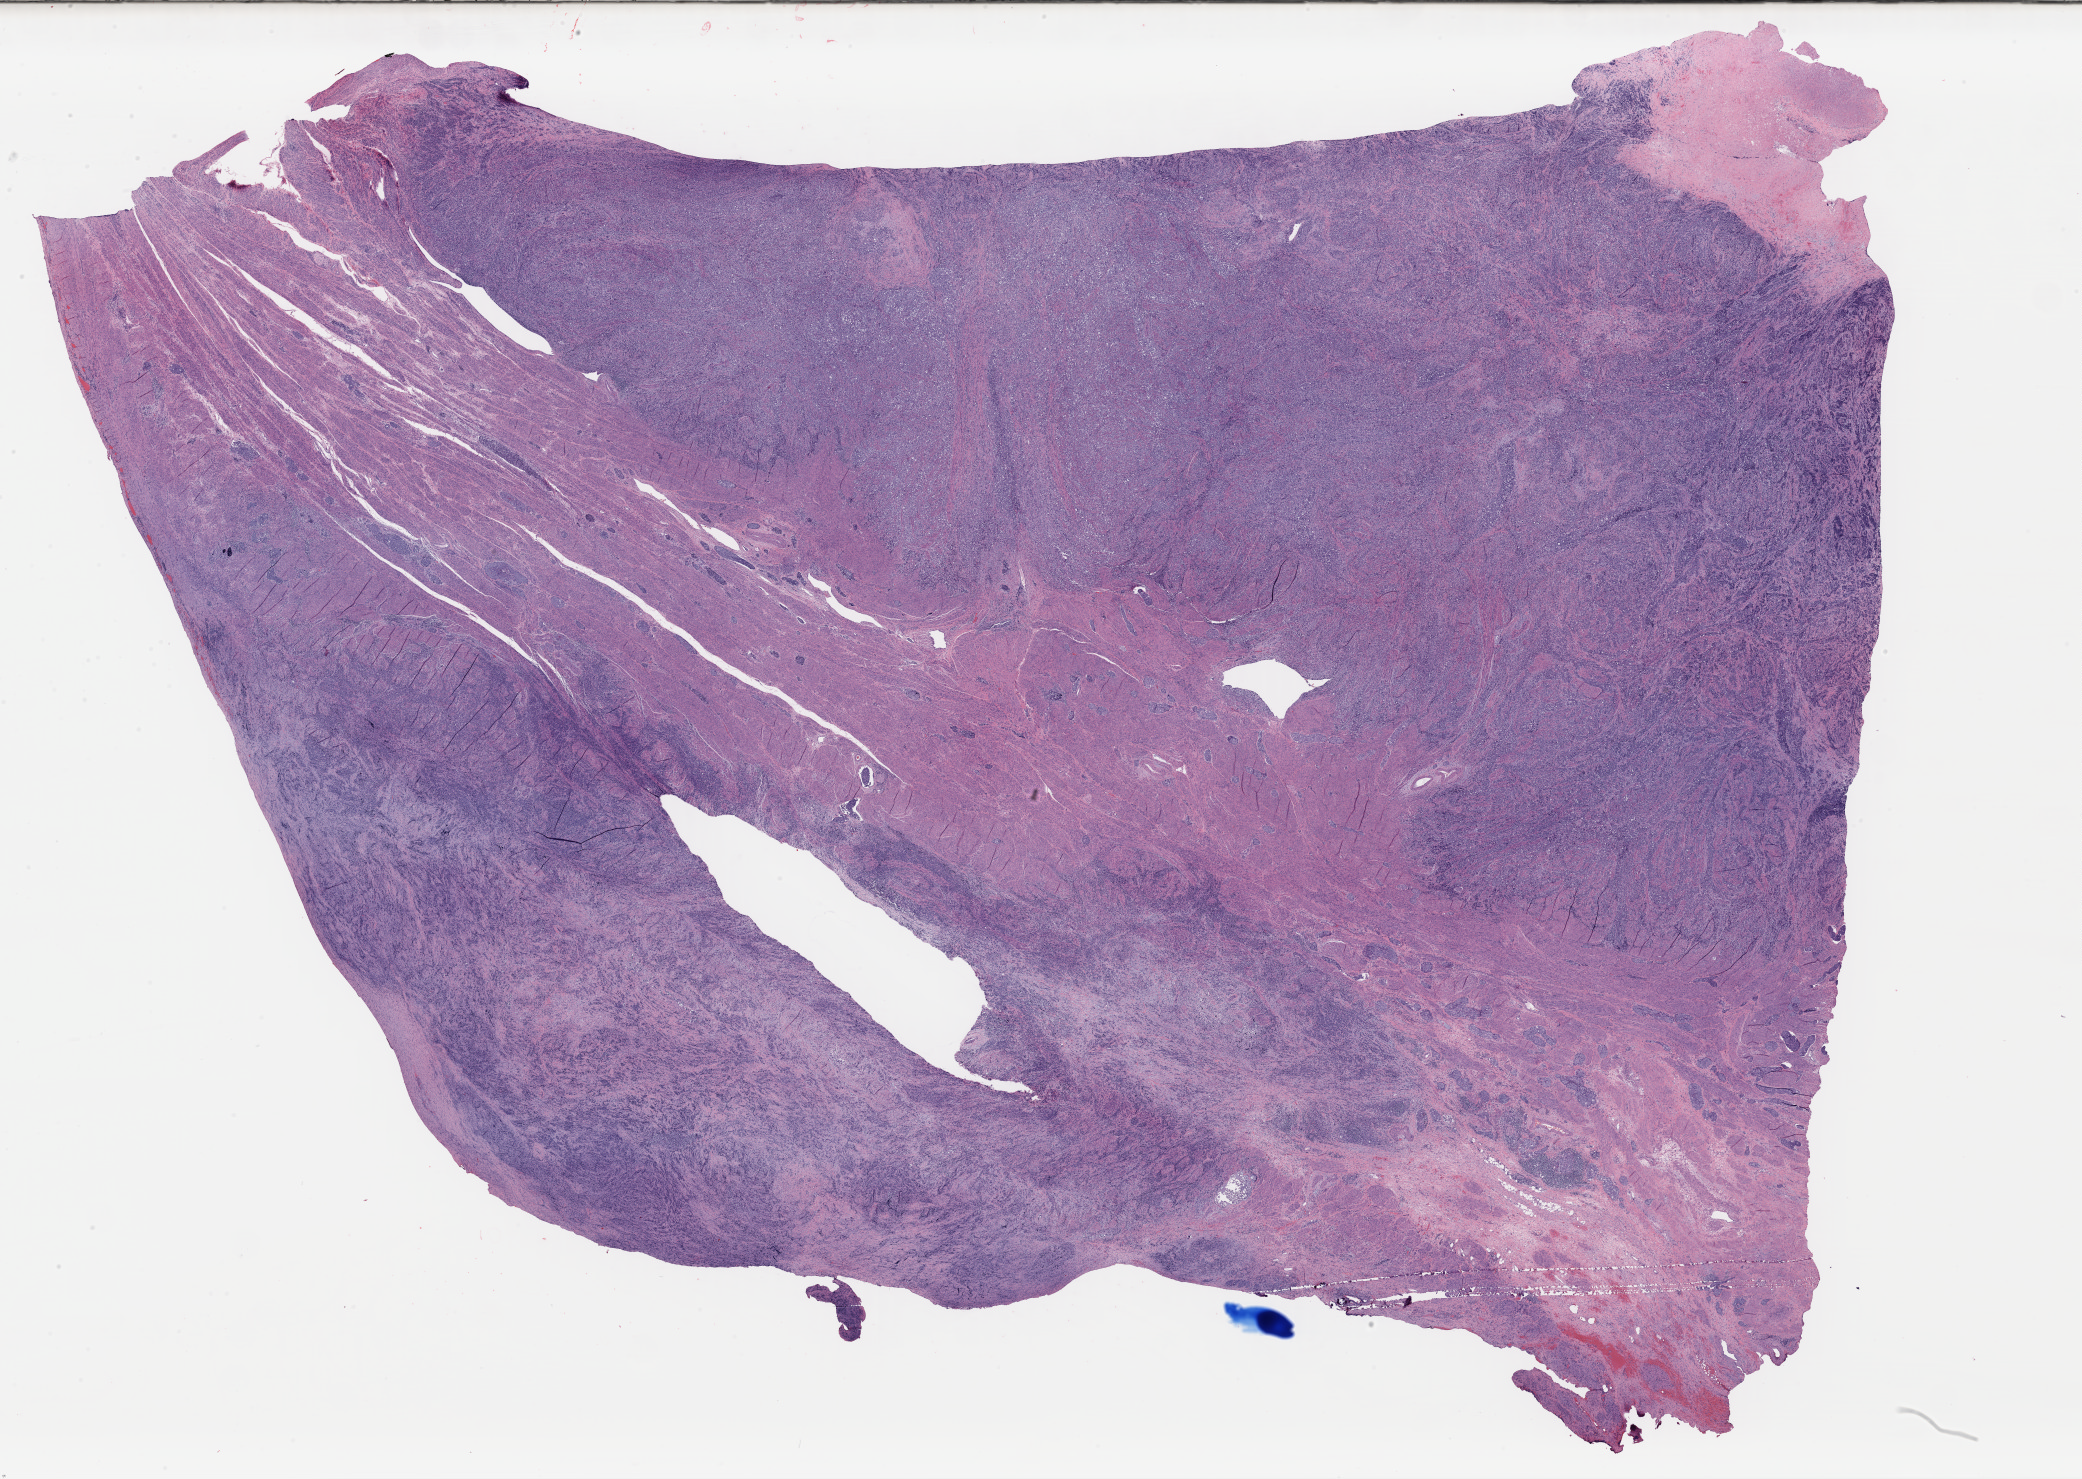
Digitized H&E-stained tissue section (whole slide) — shown as a low-resolution overview of the whole scanned area (about 32.9 x 23.4 mm, acquisition: 40x scan); formalin-fixed paraffin-embedded (FFPE) diagnostic section; uterus, primary tumour sample. Female patient; age at initial diagnosis 63 years. Histologic grade: G3 (poorly differentiated).
• diagnosis: Endometrioid adenocarcinoma, NOS (endometrium)
• FIGO stage: IIIB